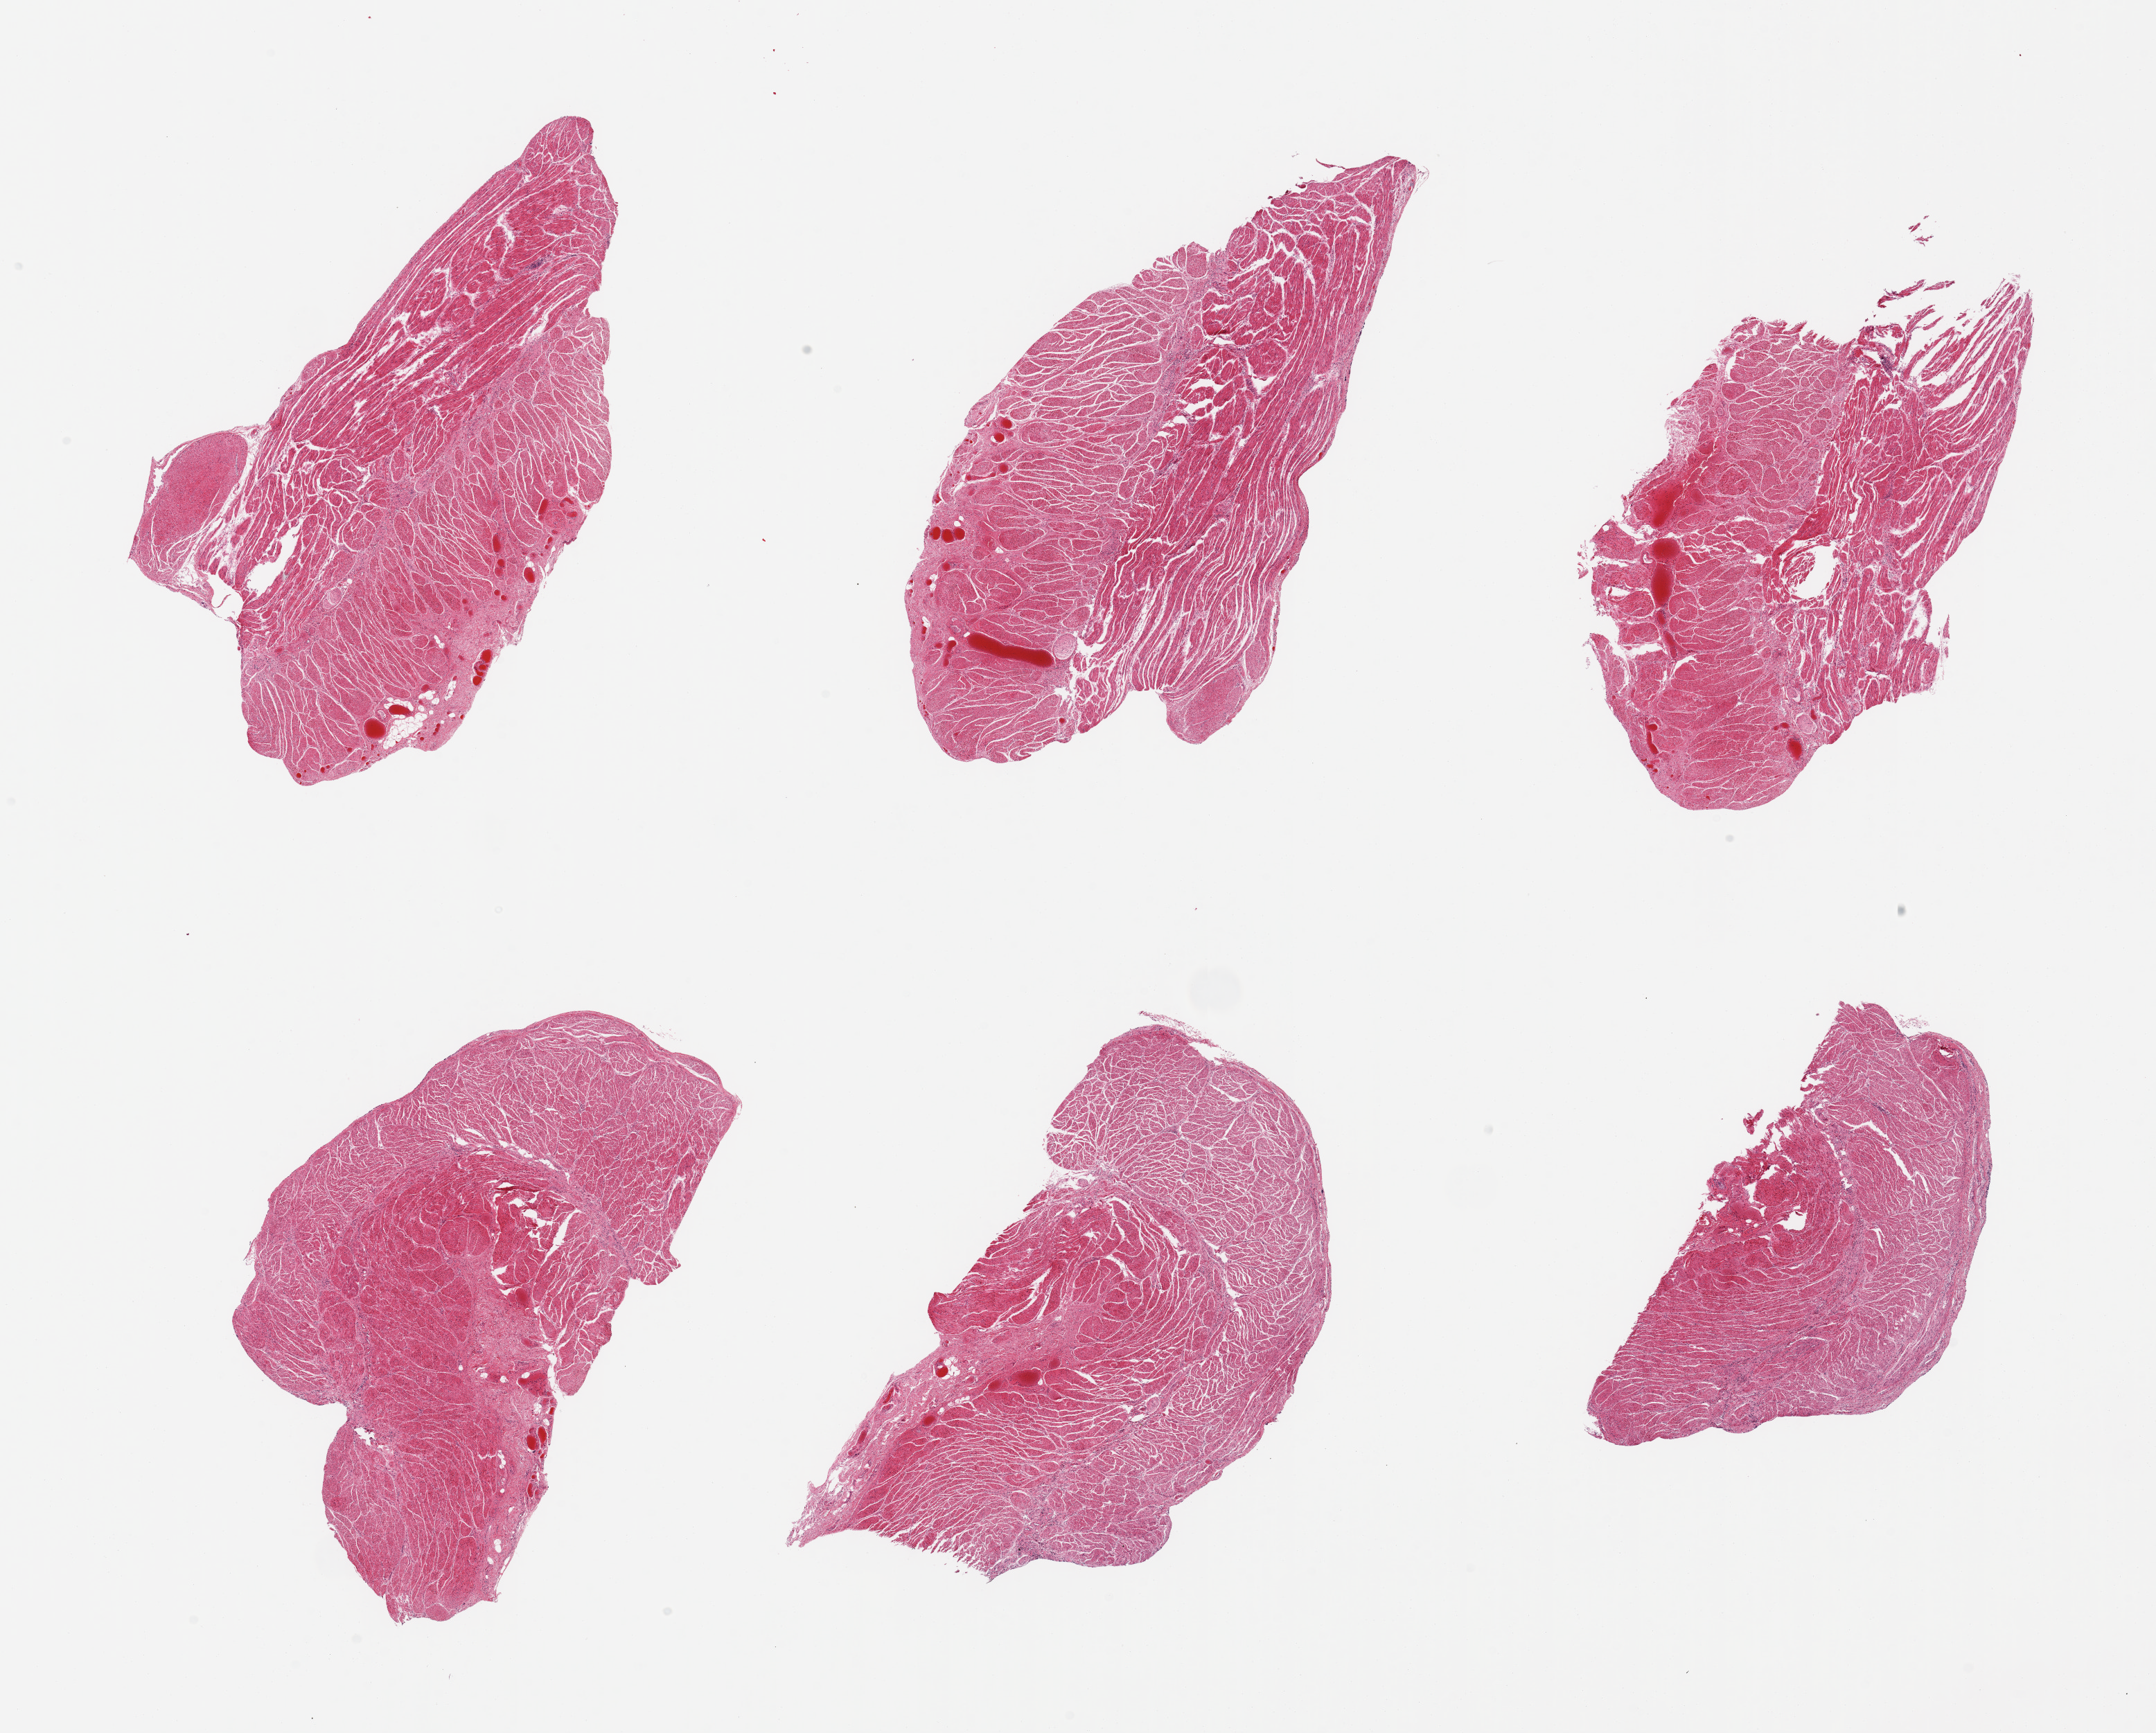
Whole-slide image, hematoxylin and eosin (H&E) stain, low-resolution overview of the scanned area, about 24.6 x 19.8 mm, PAXgene-fixed paraffin-embedded (PFPE) section, sampled site (target tissue): gastroesophageal junction, donor tissue sample. Female donor.
Reviewer comment on this tissue sample: 6 pieces; well dissected.